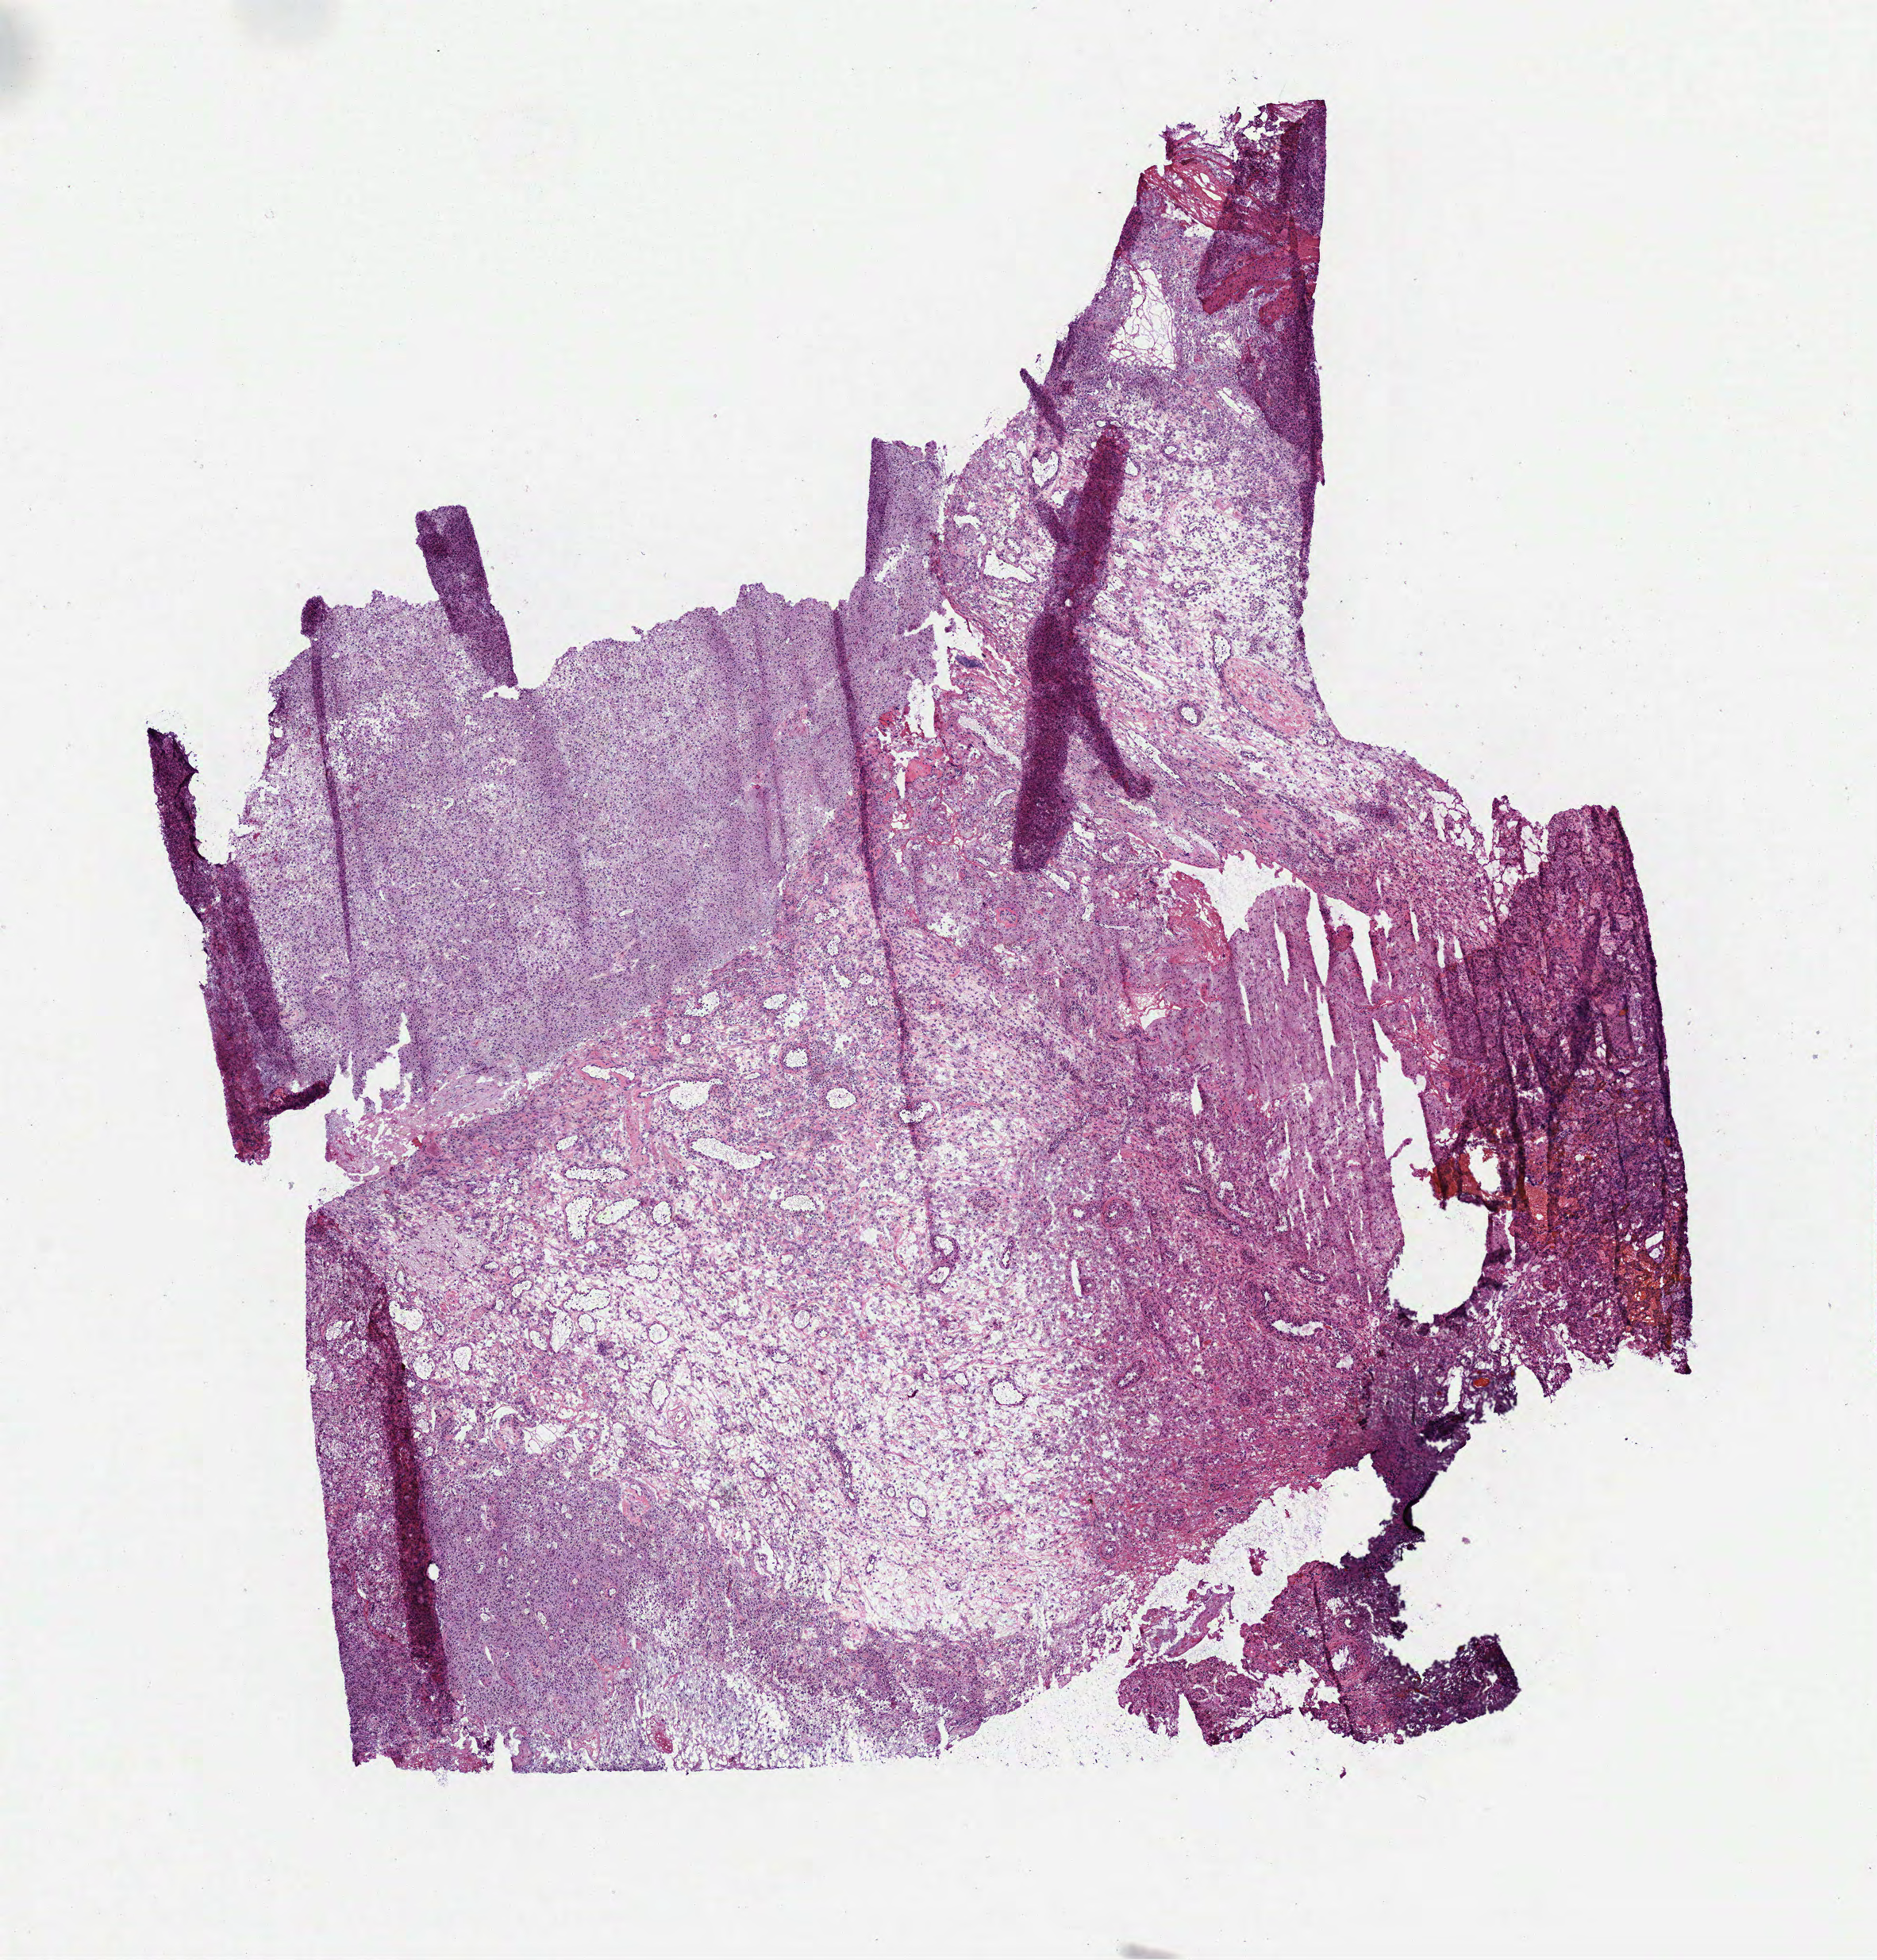
Digitized H&E tissue section (whole slide), whole scanned area (about 9.5 x 10.0 mm) shown as a low-resolution overview. Frozen section from the bottom of the tissue portion. Primary tumour sample from the brain. Patient: male, age at initial diagnosis 66 years.
Diagnosis: Oligodendroglioma, anaplastic (cerebrum).